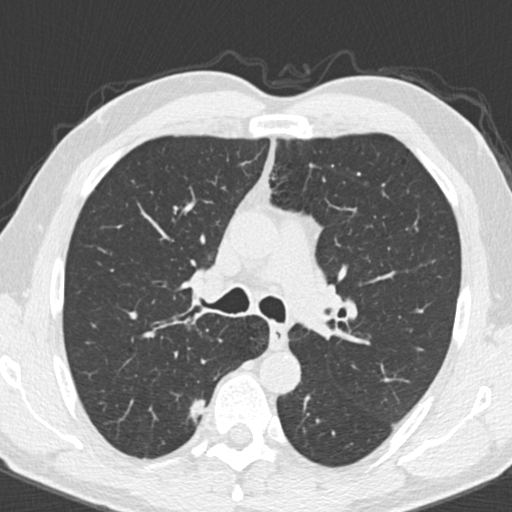
Low-dose screening chest CT, one axial slice; position 129 of 192 along the scan axis; reconstruction kernel B30f; 120 kVp; lung window (W 1500 / L -600 HU); 2 mm slice thickness; 512 × 512 image matrix, field of view 307 × 307 mm.
Structures marked on this image (outlined manually by an expert reader):
- lesion 1 (tumor, upper lobe of right lung): bounding box <188,398,207,423> (left, top, right, bottom; pixels)